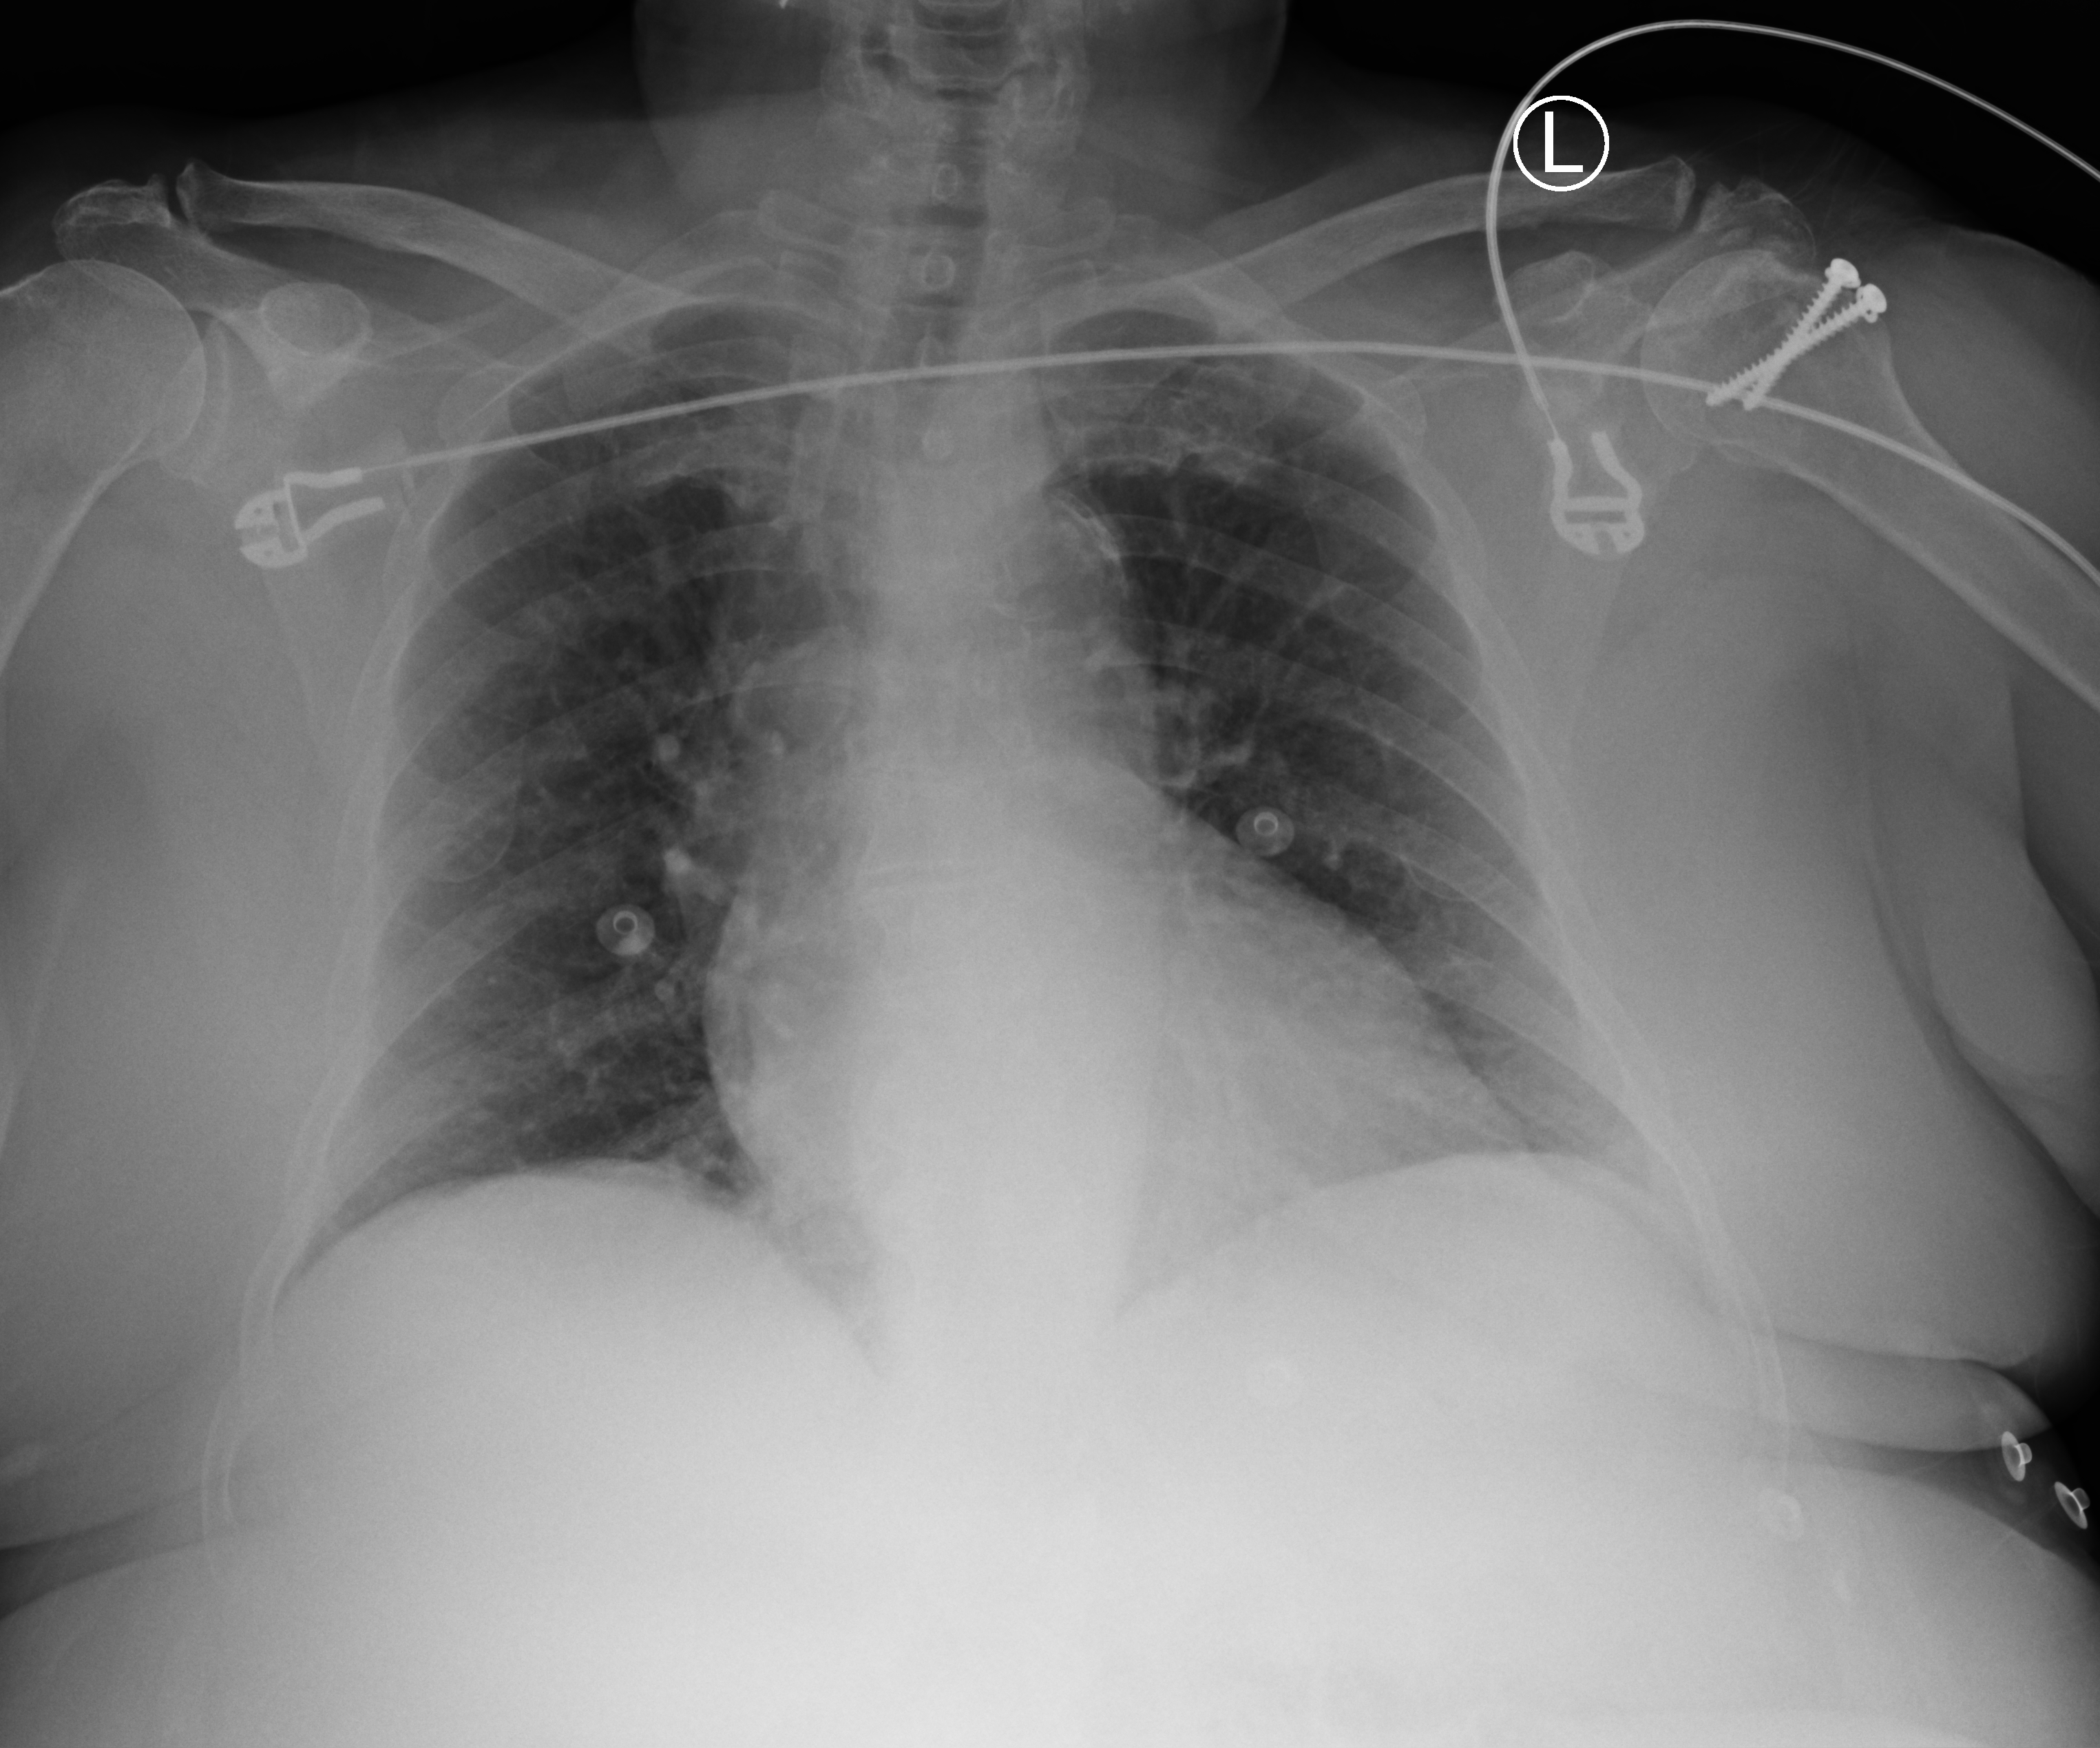
Chest X-ray (portable); anteroposterior (AP) projection. Female patient hospitalised with COVID-19, age 60–74 years.
Hospital-stay facts (about this admission, not read from this image; timing relative to this image not recorded): admitted to intensive care during this hospital stay: no.